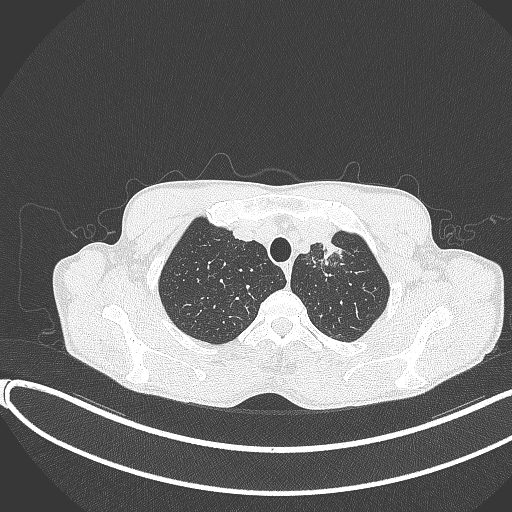
Chest CT, one axial slice. Position 333 of 374 along the scan axis. 120 kVp. Lung window (W 1500 / L -600 HU). 512 × 512 image matrix, field of view 400 × 400 mm. Male patient, age 58 years. Case-level facts recorded for this patient, not image findings: clinical TNM (as recorded): T1c N1 M0.
Outlined on this slice (bounding box drawn by a radiologist):
- lung tumour (recorded histology: adenocarcinoma): bounding box (x1, y1, x2, y2) in pixels: (320, 233, 342, 264)